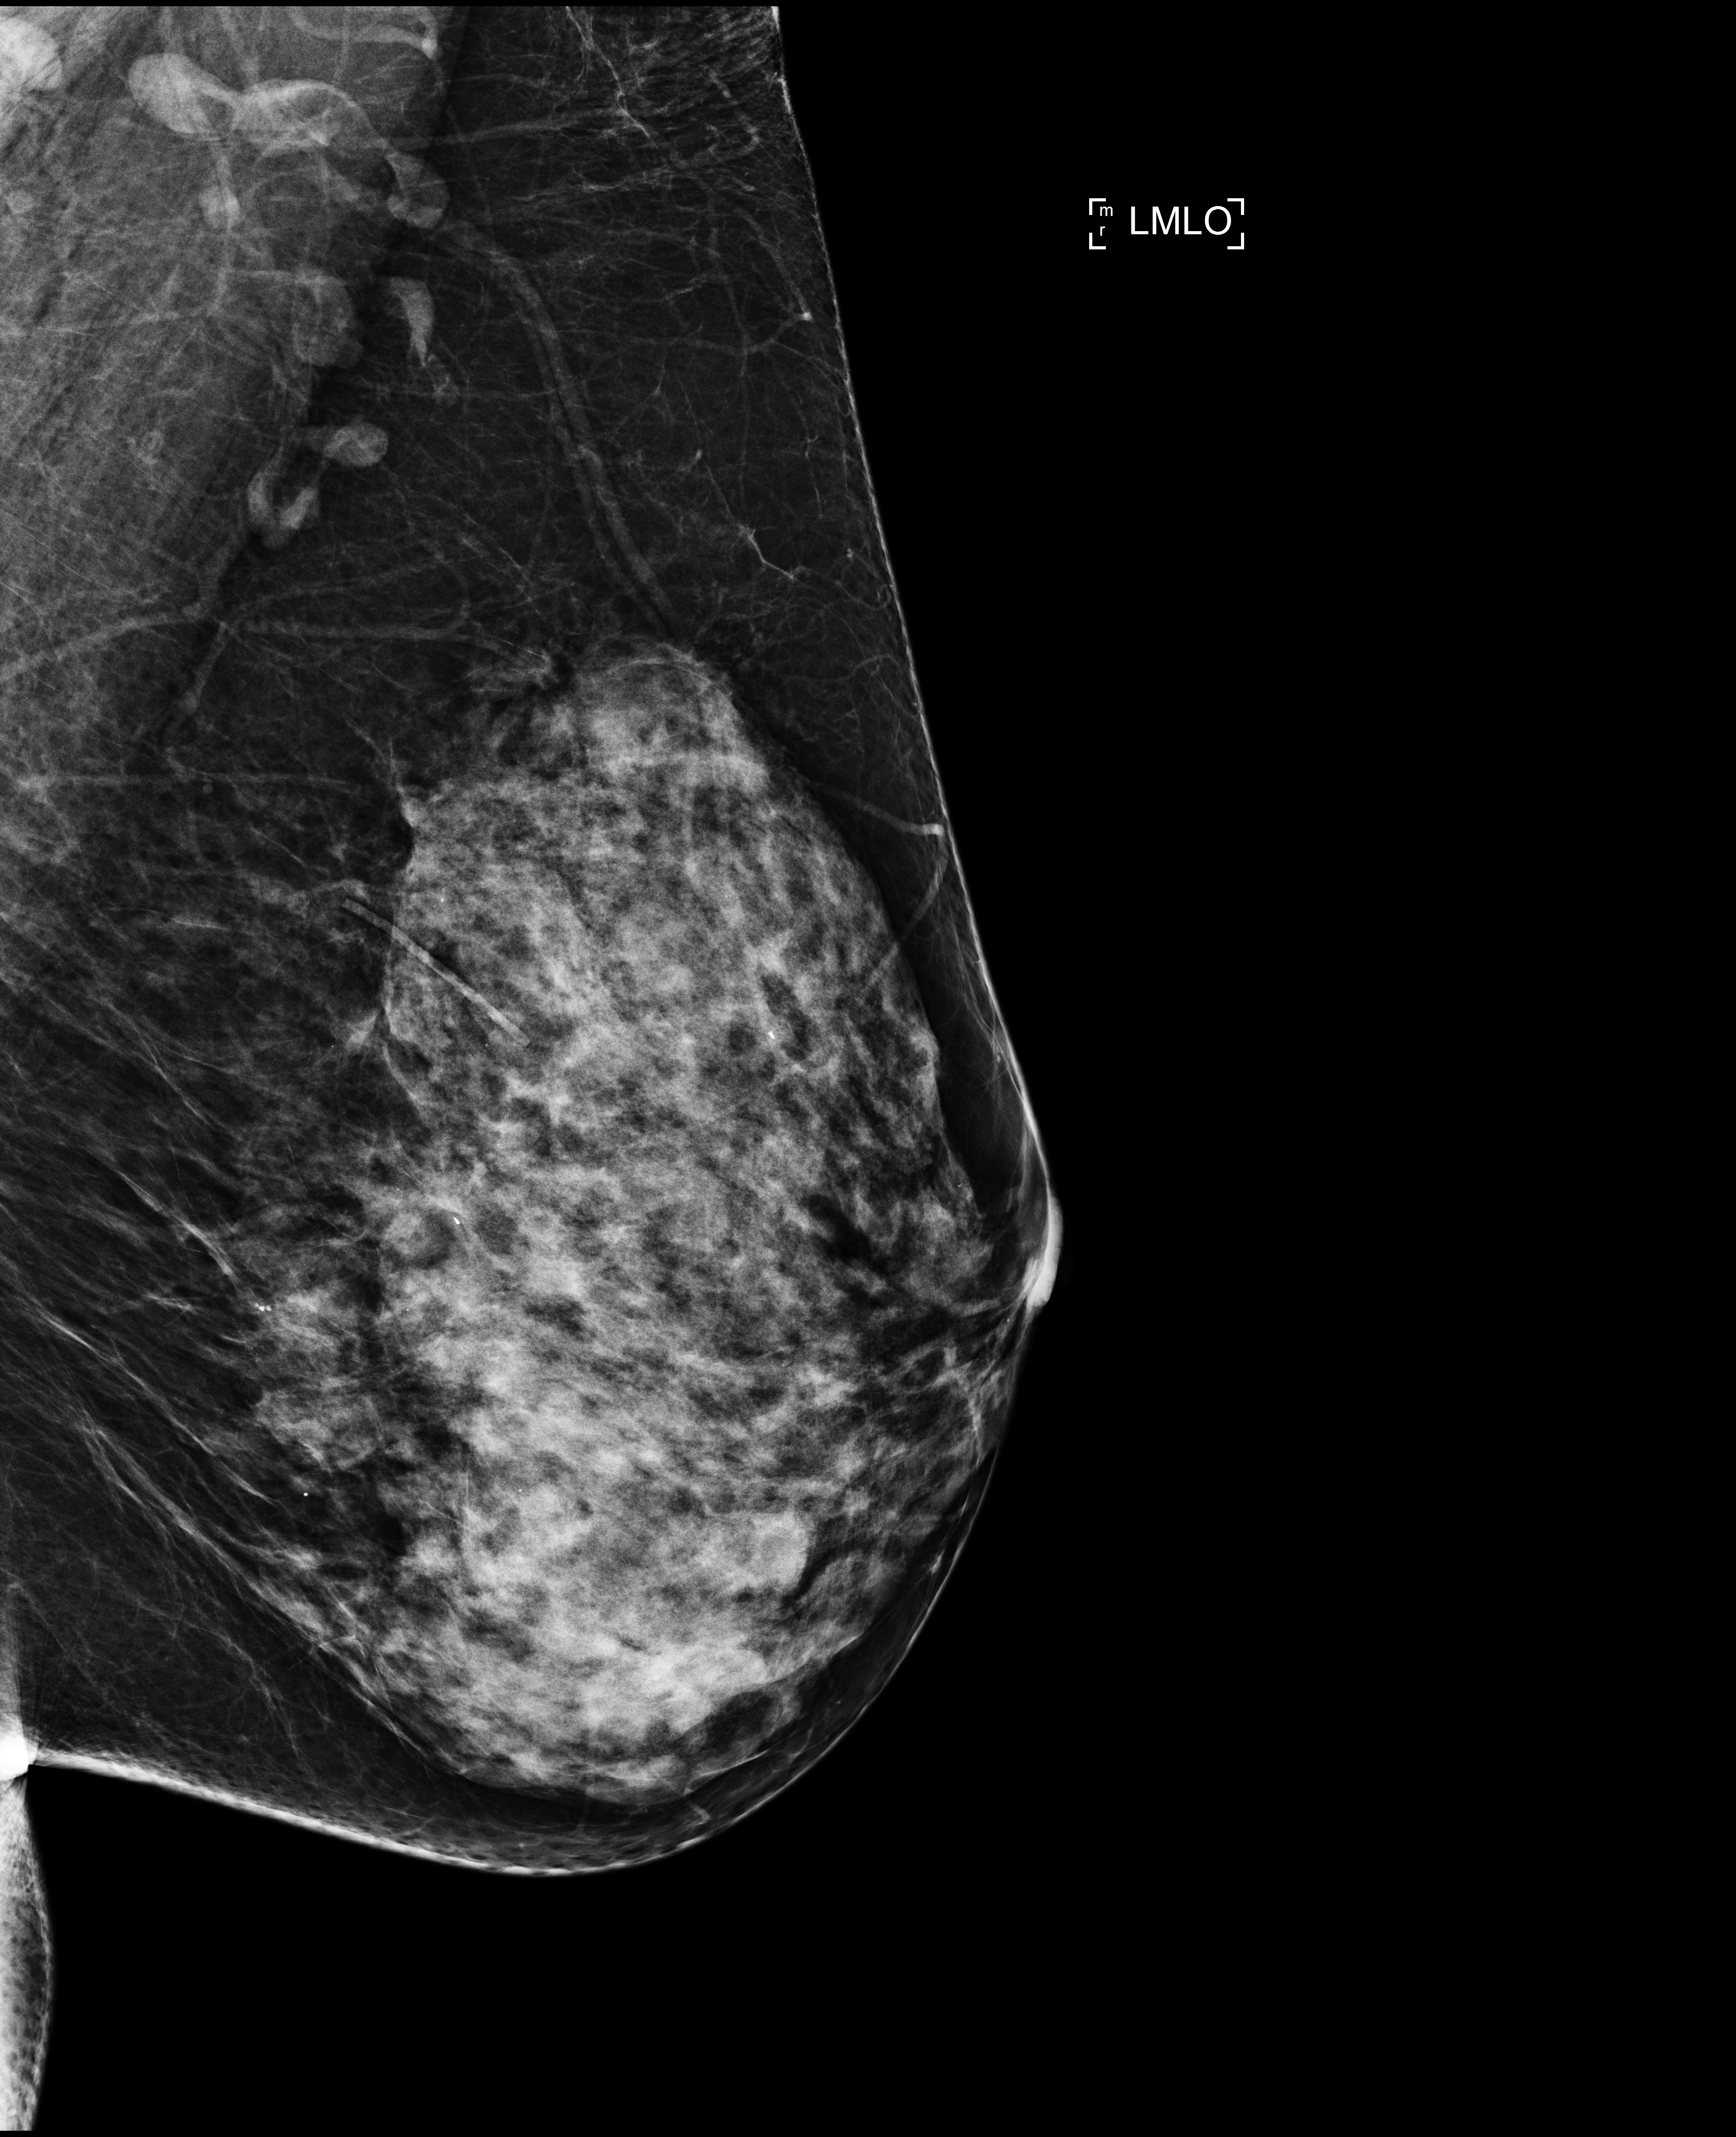
Screening examination; system: Selenia Dimensions. Patient: female, 57 years.
Image type: full-field digital mammogram. Breast: left. Projection: MLO view.